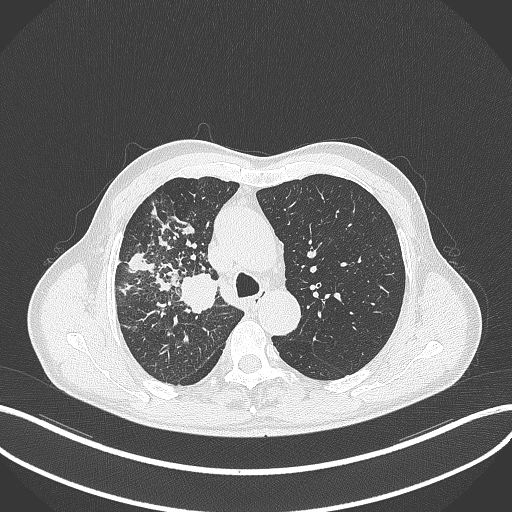
Chest CT, one axial slice; slice 340 of 490 in the series (ordered by position); reconstruction kernel B70f; 120 kVp; lung window (W 1500 / L -600 HU); 1 mm slice thickness; 512 × 512 image matrix. Male patient, age 69 years. Case-level facts recorded for this patient, not image findings: clinical TNM (as recorded): T2a N0 M0.
Annotated regions visible in this slice (bounding box drawn by a radiologist):
- lung tumour (recorded histology: adenocarcinoma): bounding box (x1, y1, x2, y2) in pixels: (178, 271, 221, 313)